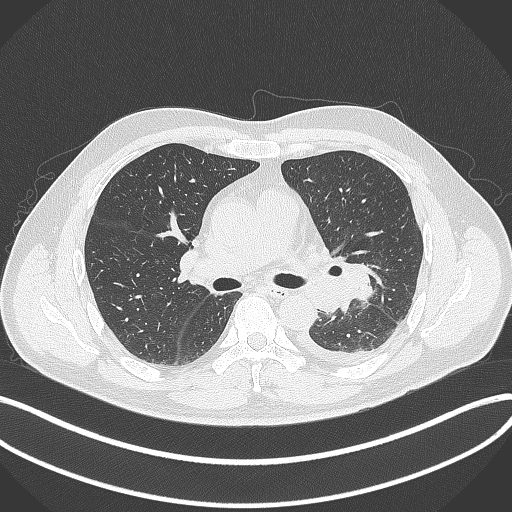
Chest CT, one axial slice; position 214 of 342 along the scan axis; 120 kVp; lung window (W 1500 / L -600 HU); 512 × 512 image matrix. Male patient, age 58 years. From the clinical record (not read from this slice): clinical TNM (as recorded): T3 N1 M1b; histopathological grade: G3.
Outlined on this slice (rectangle marked by the reading radiologist):
- lung tumour (recorded histology: small cell carcinoma): bounding box [x1, y1, x2, y2] px = [342, 263, 381, 302]